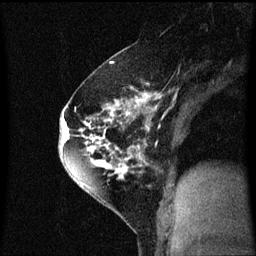
Breast MRI (dynamic contrast-enhanced), one sagittal slice. Dynamic contrast-enhanced series, image 2 of 3 at this slice position (ordered by acquisition). 1.5 T. TE 4.2 ms, TR 8.4 ms. 256 × 256 image matrix, field of view 200 × 200 mm. Female patient, age 60 years.
Structures marked on this image (semi-automatically segmented with operator editing):
- analysis volume of interest (the breast-tissue region the enhancement analysis was run in; not a lesion): bounding box <64,70,147,195> (left, top, right, bottom; pixels)
- tumour enhancement mask (voxels above the 70 % enhancement threshold inside the analysis volume of interest): <64,92,147,187>